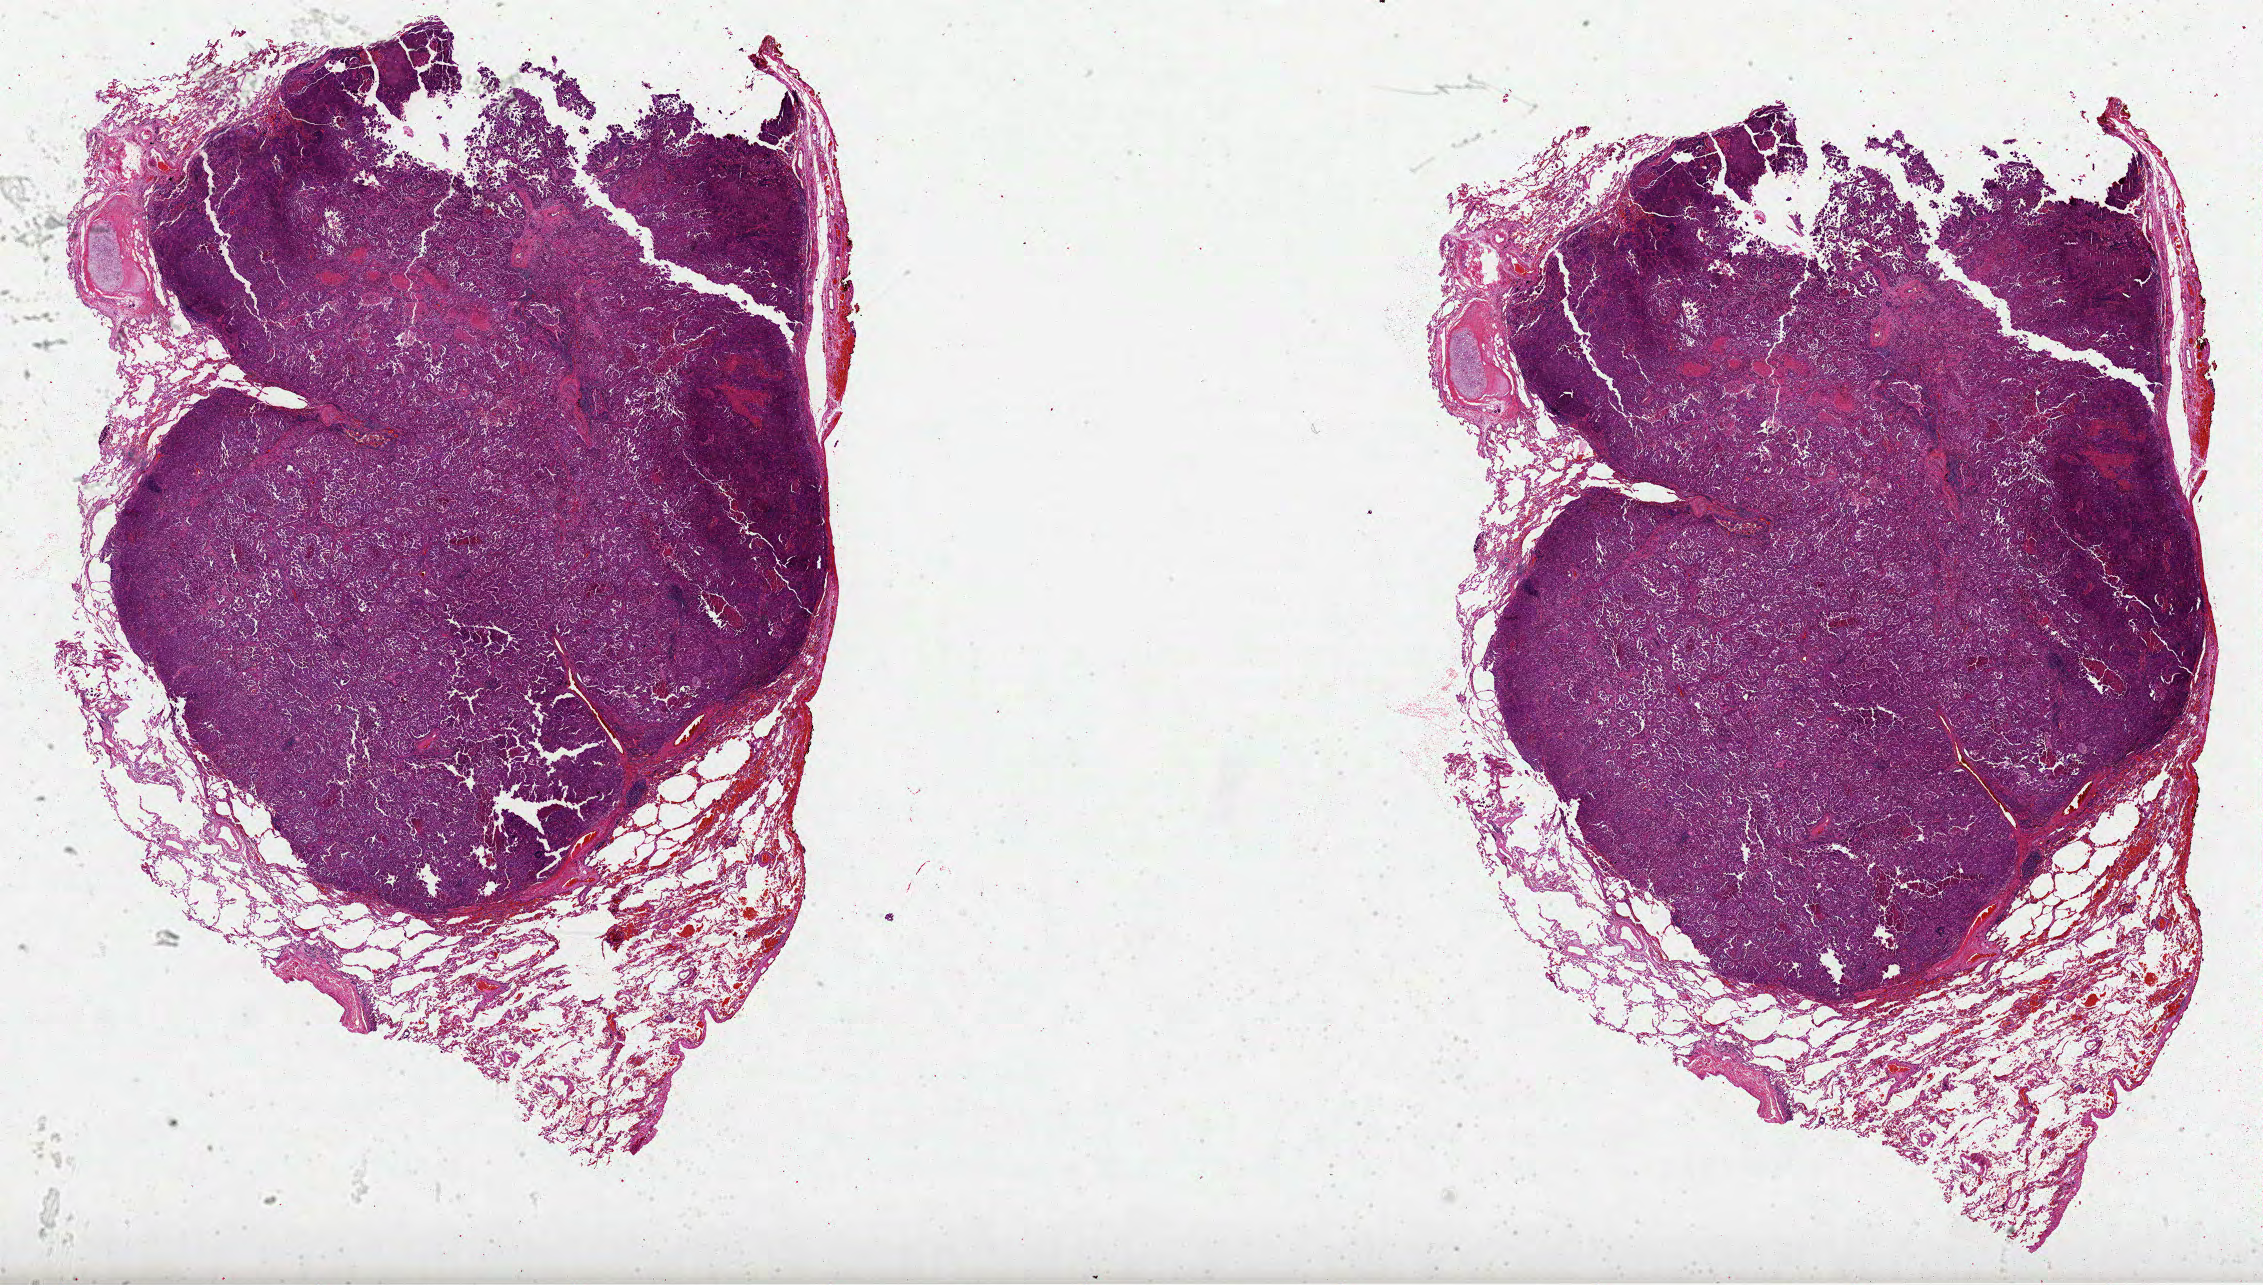
H&E whole-slide image — a low-resolution overview of the entire scanned area, about 36.5 x 20.7 mm; formalin-fixed paraffin-embedded (FFPE) diagnostic section; sample: primary tumour, lung. Patient: male, age at initial diagnosis 82 years.
• histologic diagnosis: Papillary adenocarcinoma, NOS (upper lobe, lung)
• AJCC pathologic stage: IIIA (7th edition)